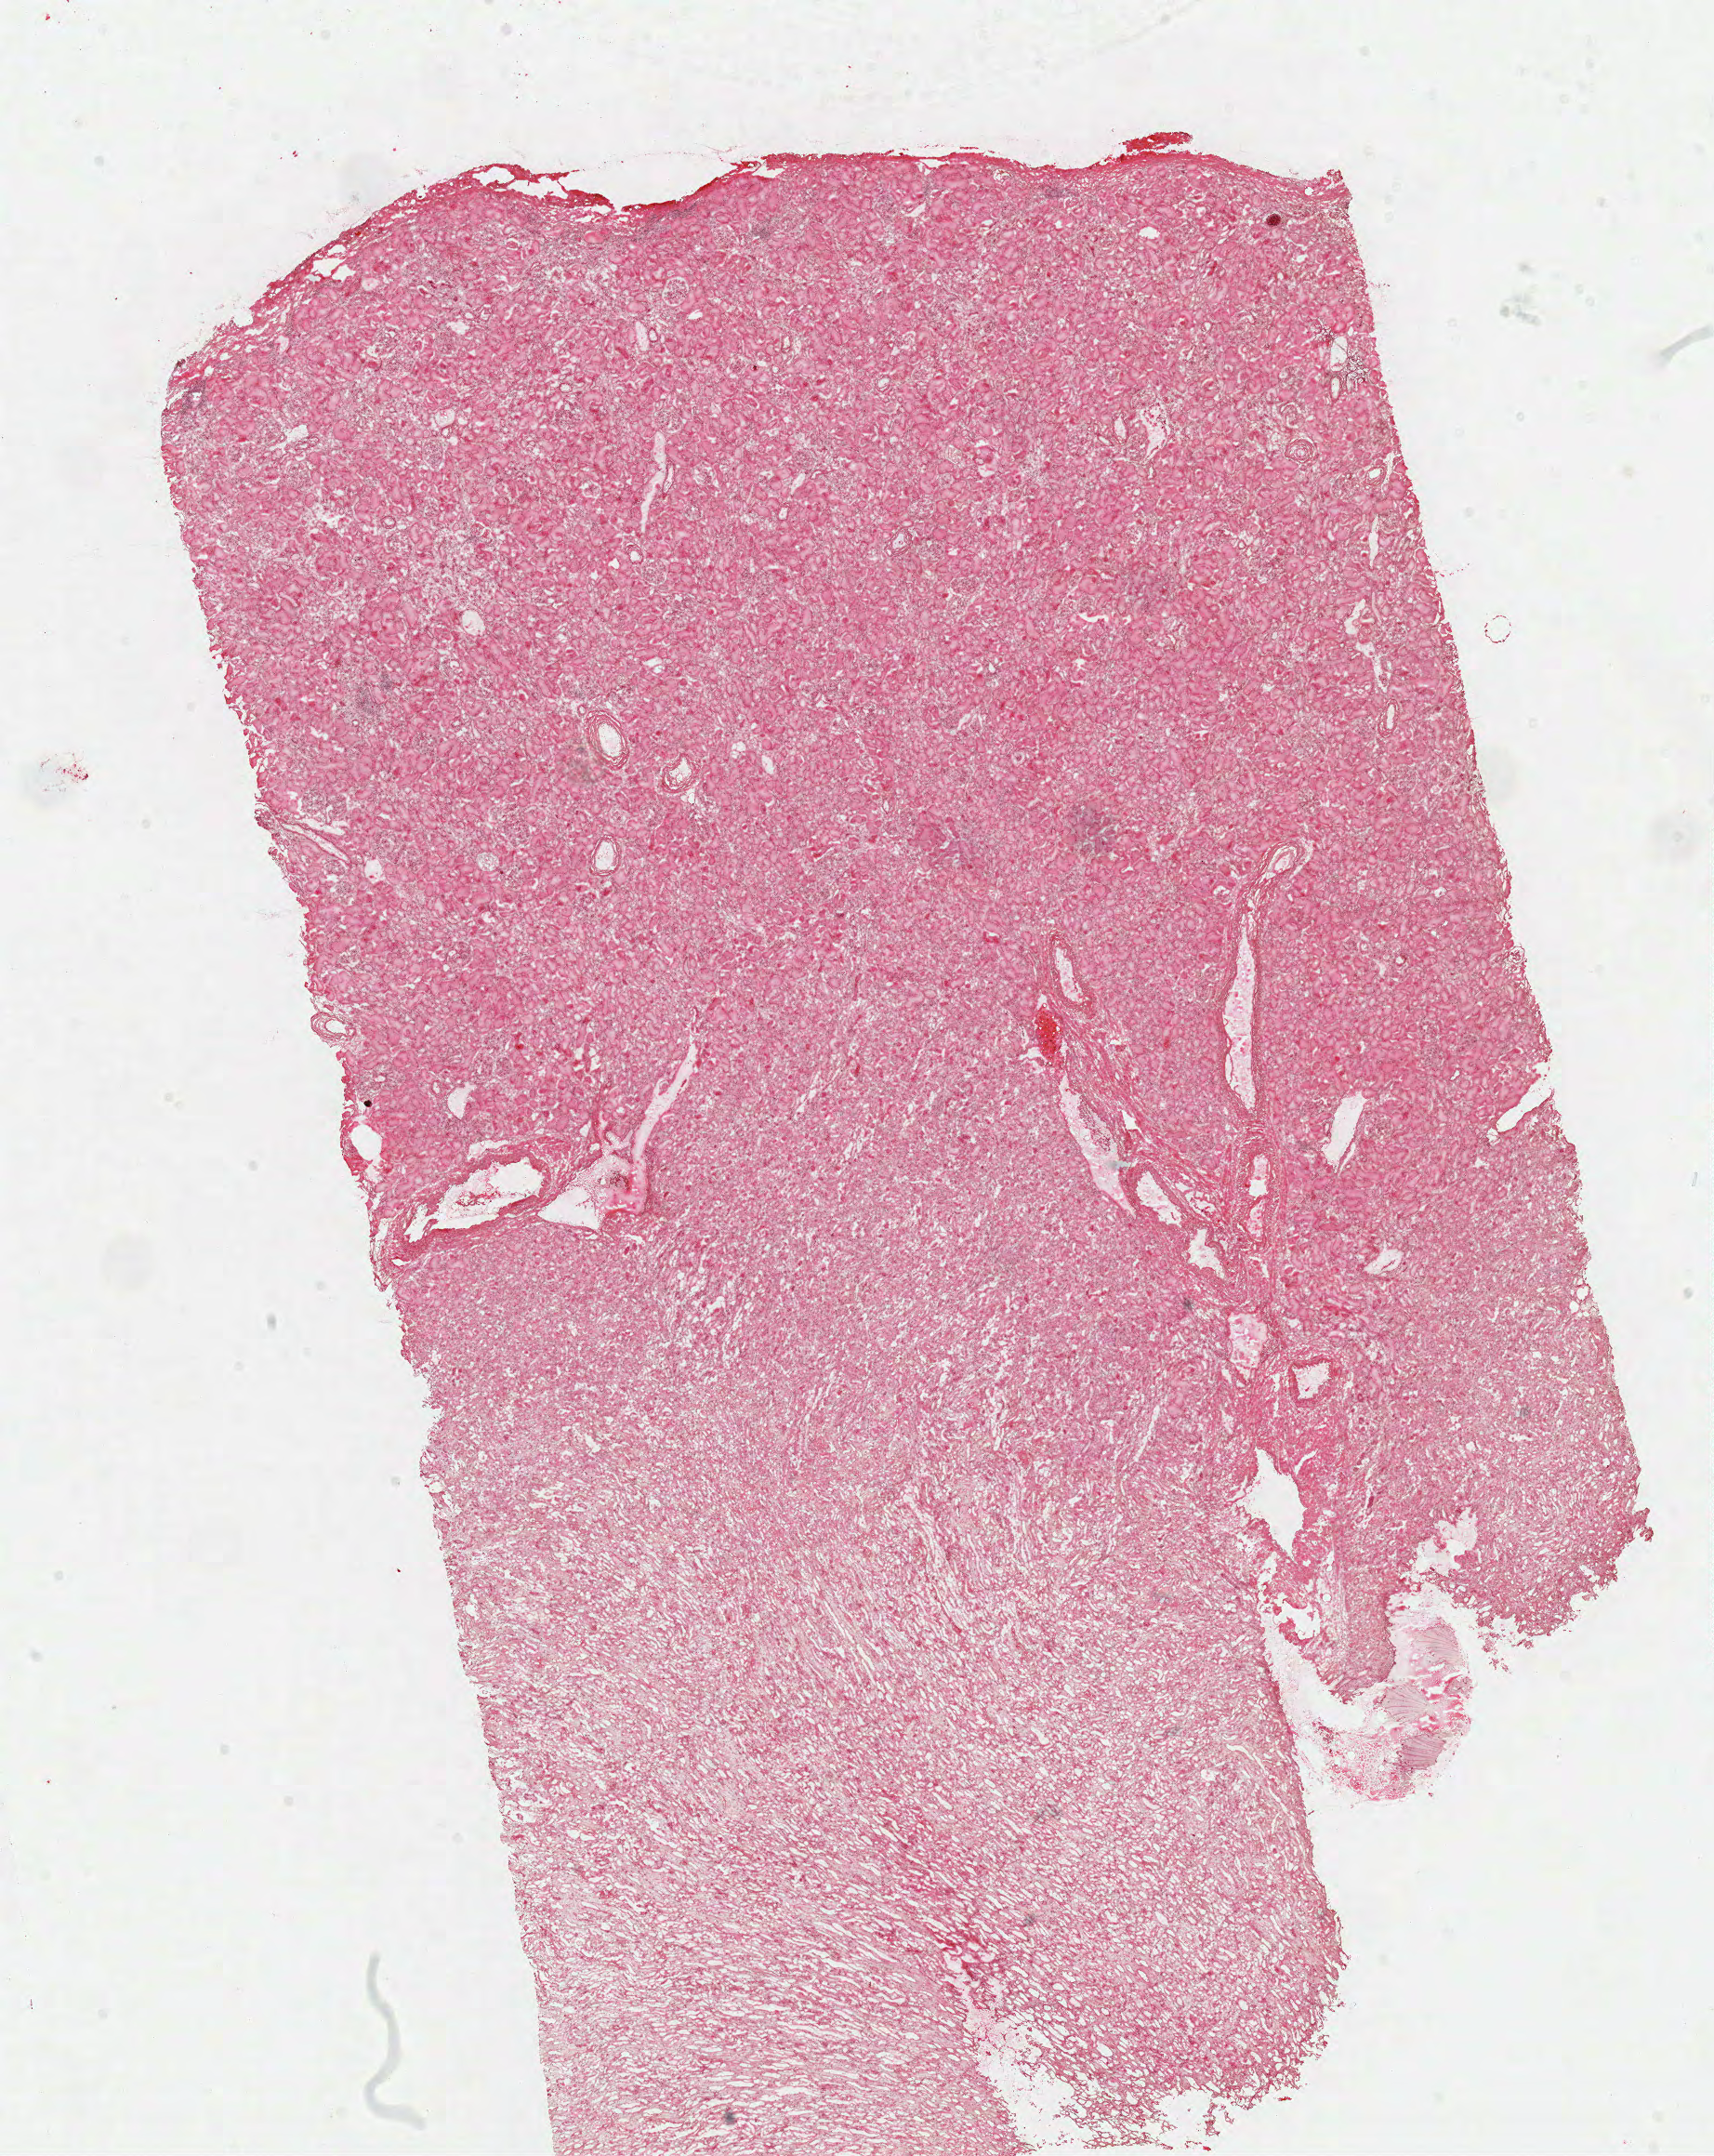
Whole-slide histology image, Hematoxylin and eosin (H&E) stained — whole scanned area (about 14.5 x 18.3 mm) shown as a low-resolution overview. Frozen section from the top of the tissue portion. Sample: solid tissue normal (non-tumour tissue), kidney. Patient: male, age at initial diagnosis 79 years.
This section: solid tissue normal sample (biorepository sample class). Patient diagnosis: Papillary adenocarcinoma, NOS.